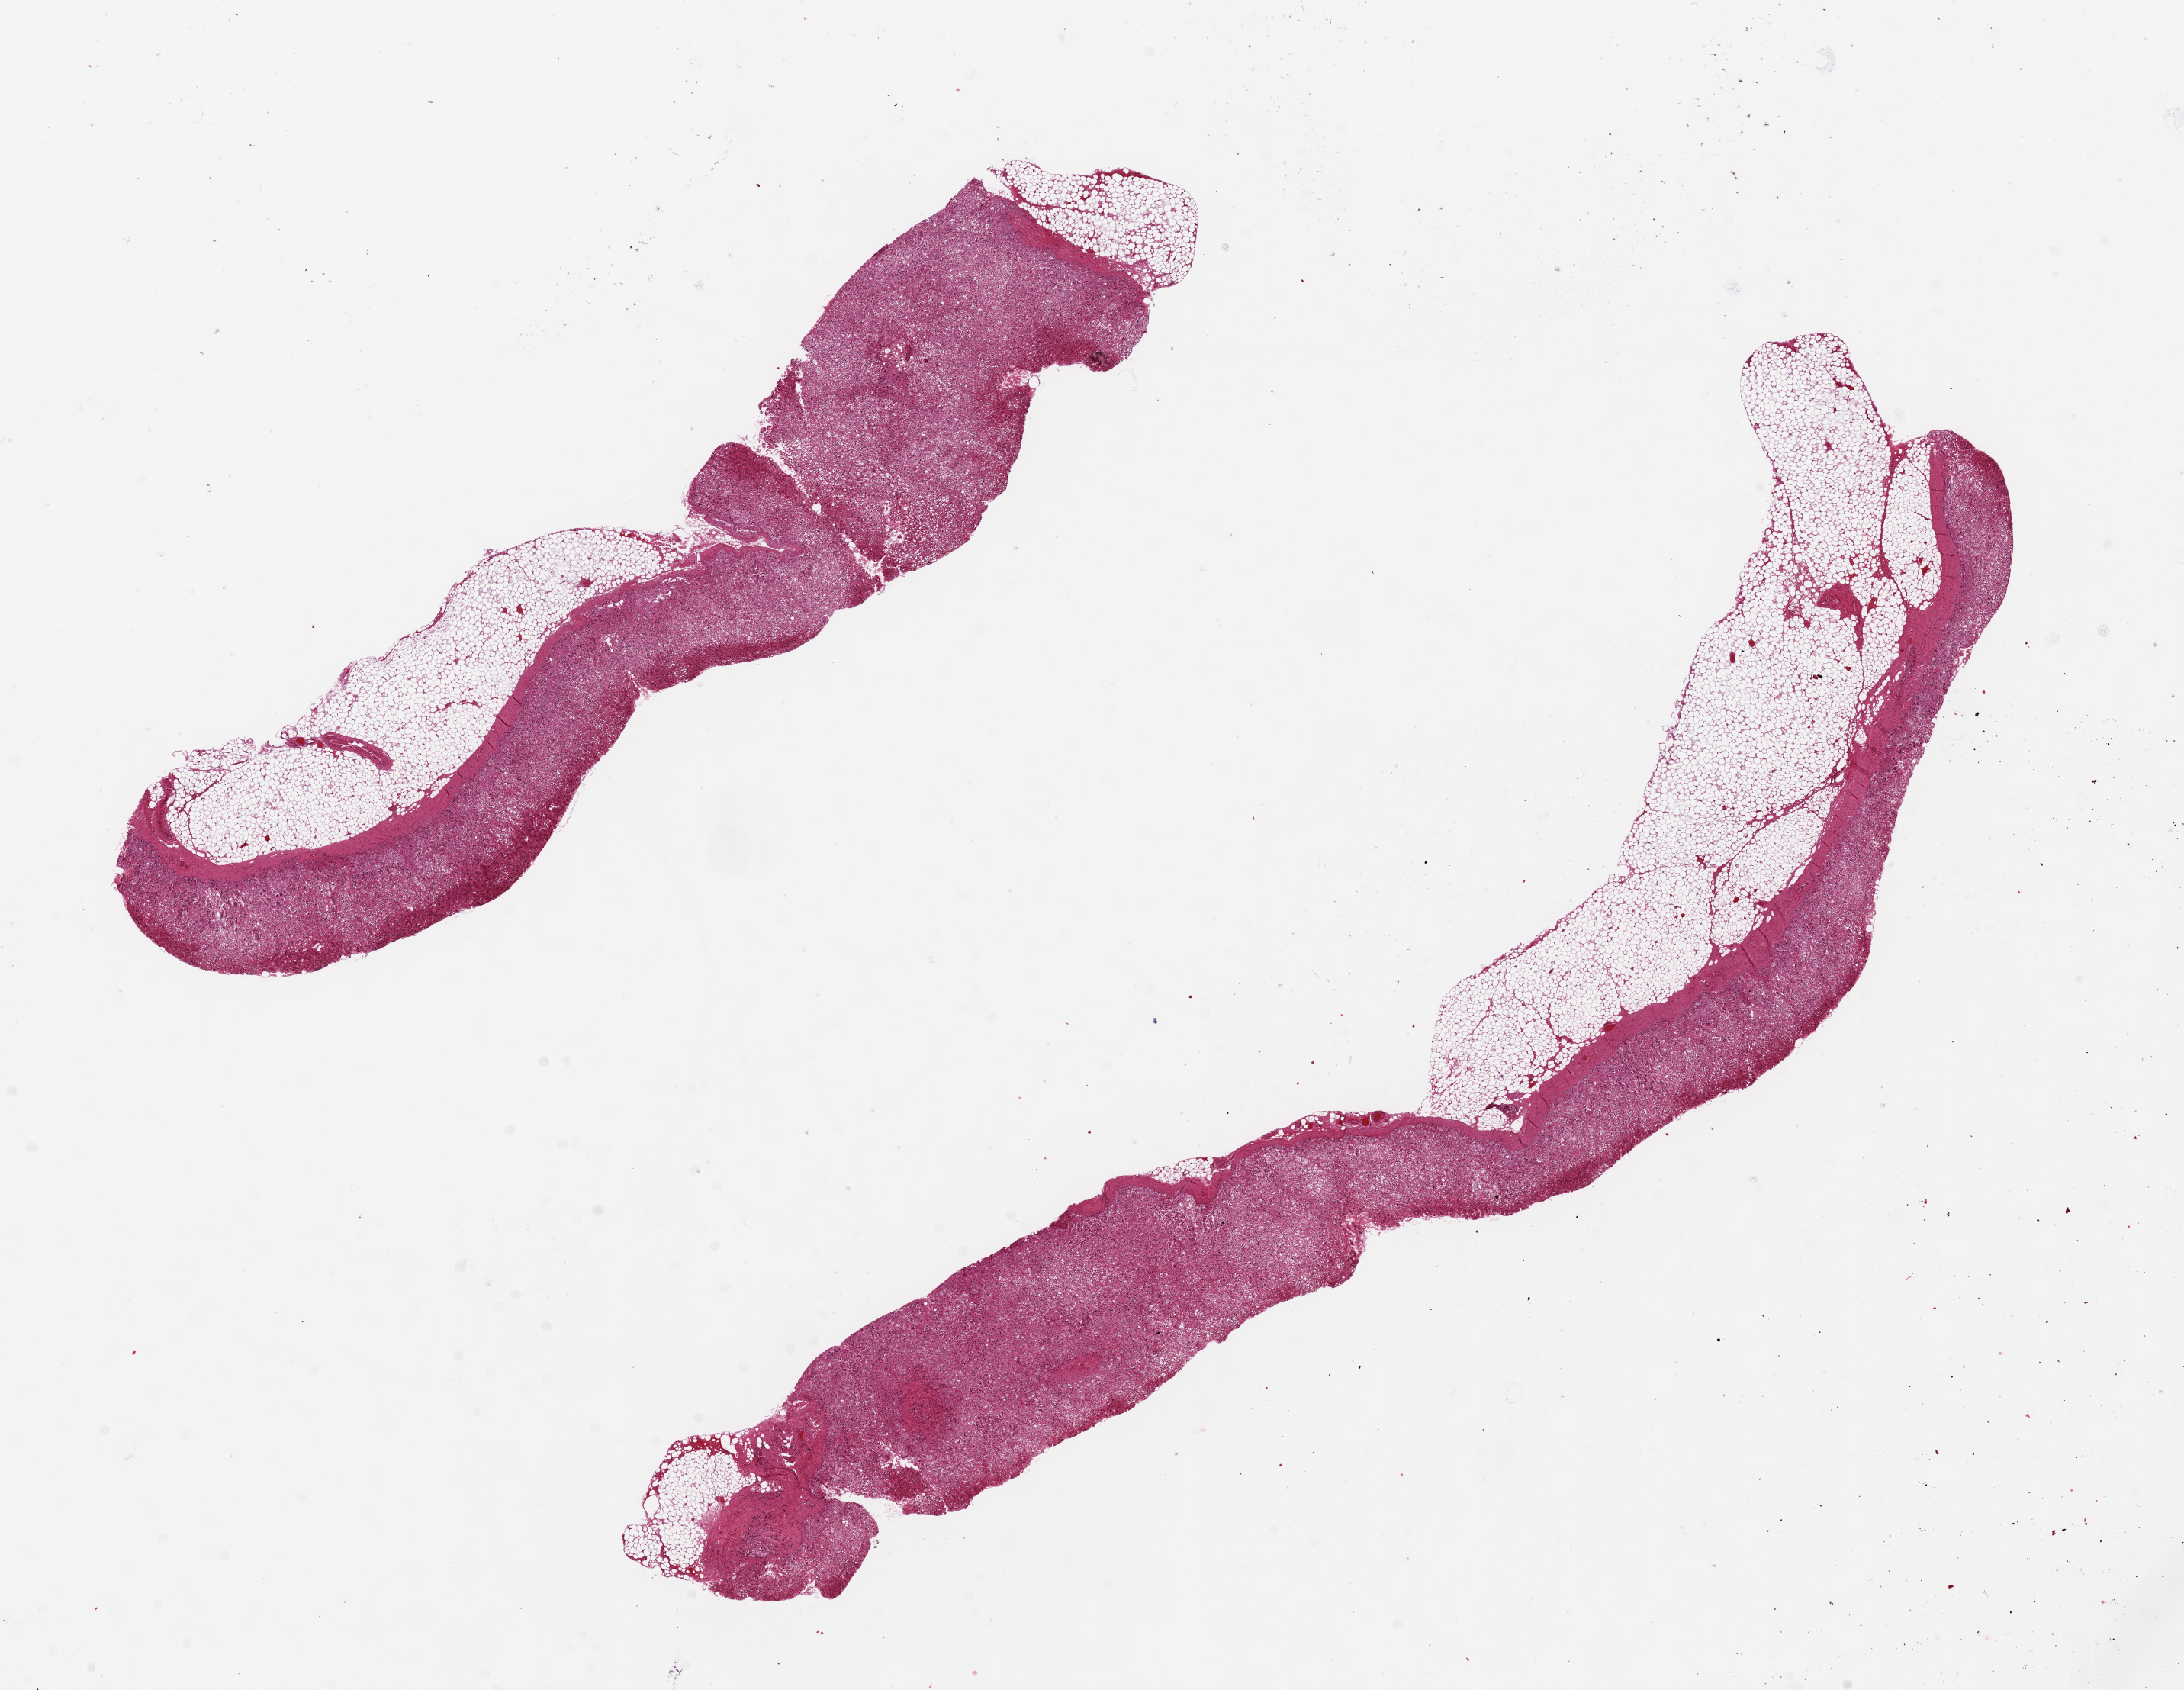
H&E whole-slide image — whole scanned area (about 22.6 x 17.5 mm, from a 20x scan) shown as a low-resolution overview, PAXgene-fixed, paraffin-embedded tissue, target tissue: adrenal gland, donor tissue sample. Male donor.
Reviewer comment on this tissue sample: 2 pieces ~14x2mm, all cortex, each about 30-40% fat.